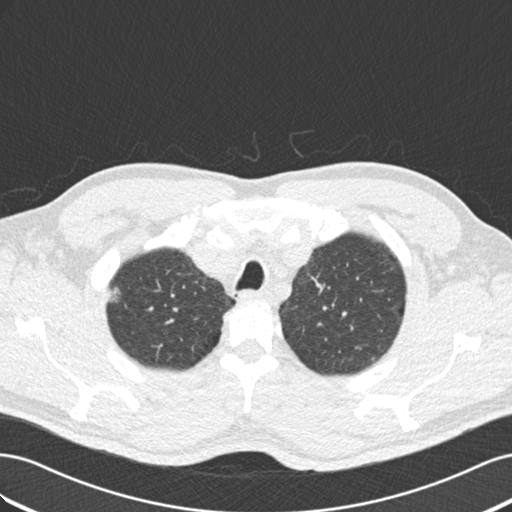
Low-dose screening chest CT, one axial slice; slice 152 of 187 in the series (ordered by position); reconstruction kernel B30f; lung window (W 1500 / L -600 HU); 2 mm slice thickness; 512 × 512 image matrix.
Outlined on this slice (manually delineated by an expert):
- lesion 1 (tumor, upper lobe of right lung): bounding box [x1, y1, x2, y2] px = [110, 287, 121, 302]